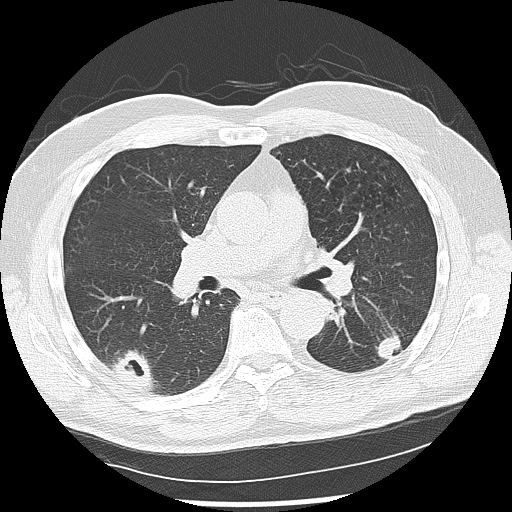
Low-dose screening chest CT, one axial slice; slice 73 of 142 in the series (ordered by position); reconstruction kernel LUNG; 120 kVp; lung window (W 1500 / L -600 HU); 2.5 mm slice thickness; 512 × 512 image matrix, field of view 360 × 360 mm.
Annotated regions visible in this slice (outlined manually by an expert reader):
- lesion 1 (nodule, lower lobe of left lung): box from (x=376, y=334) to (x=401, y=360) px
- lesion 2 (nodule, lower lobe of right lung): (x=109, y=349)–(x=157, y=392)